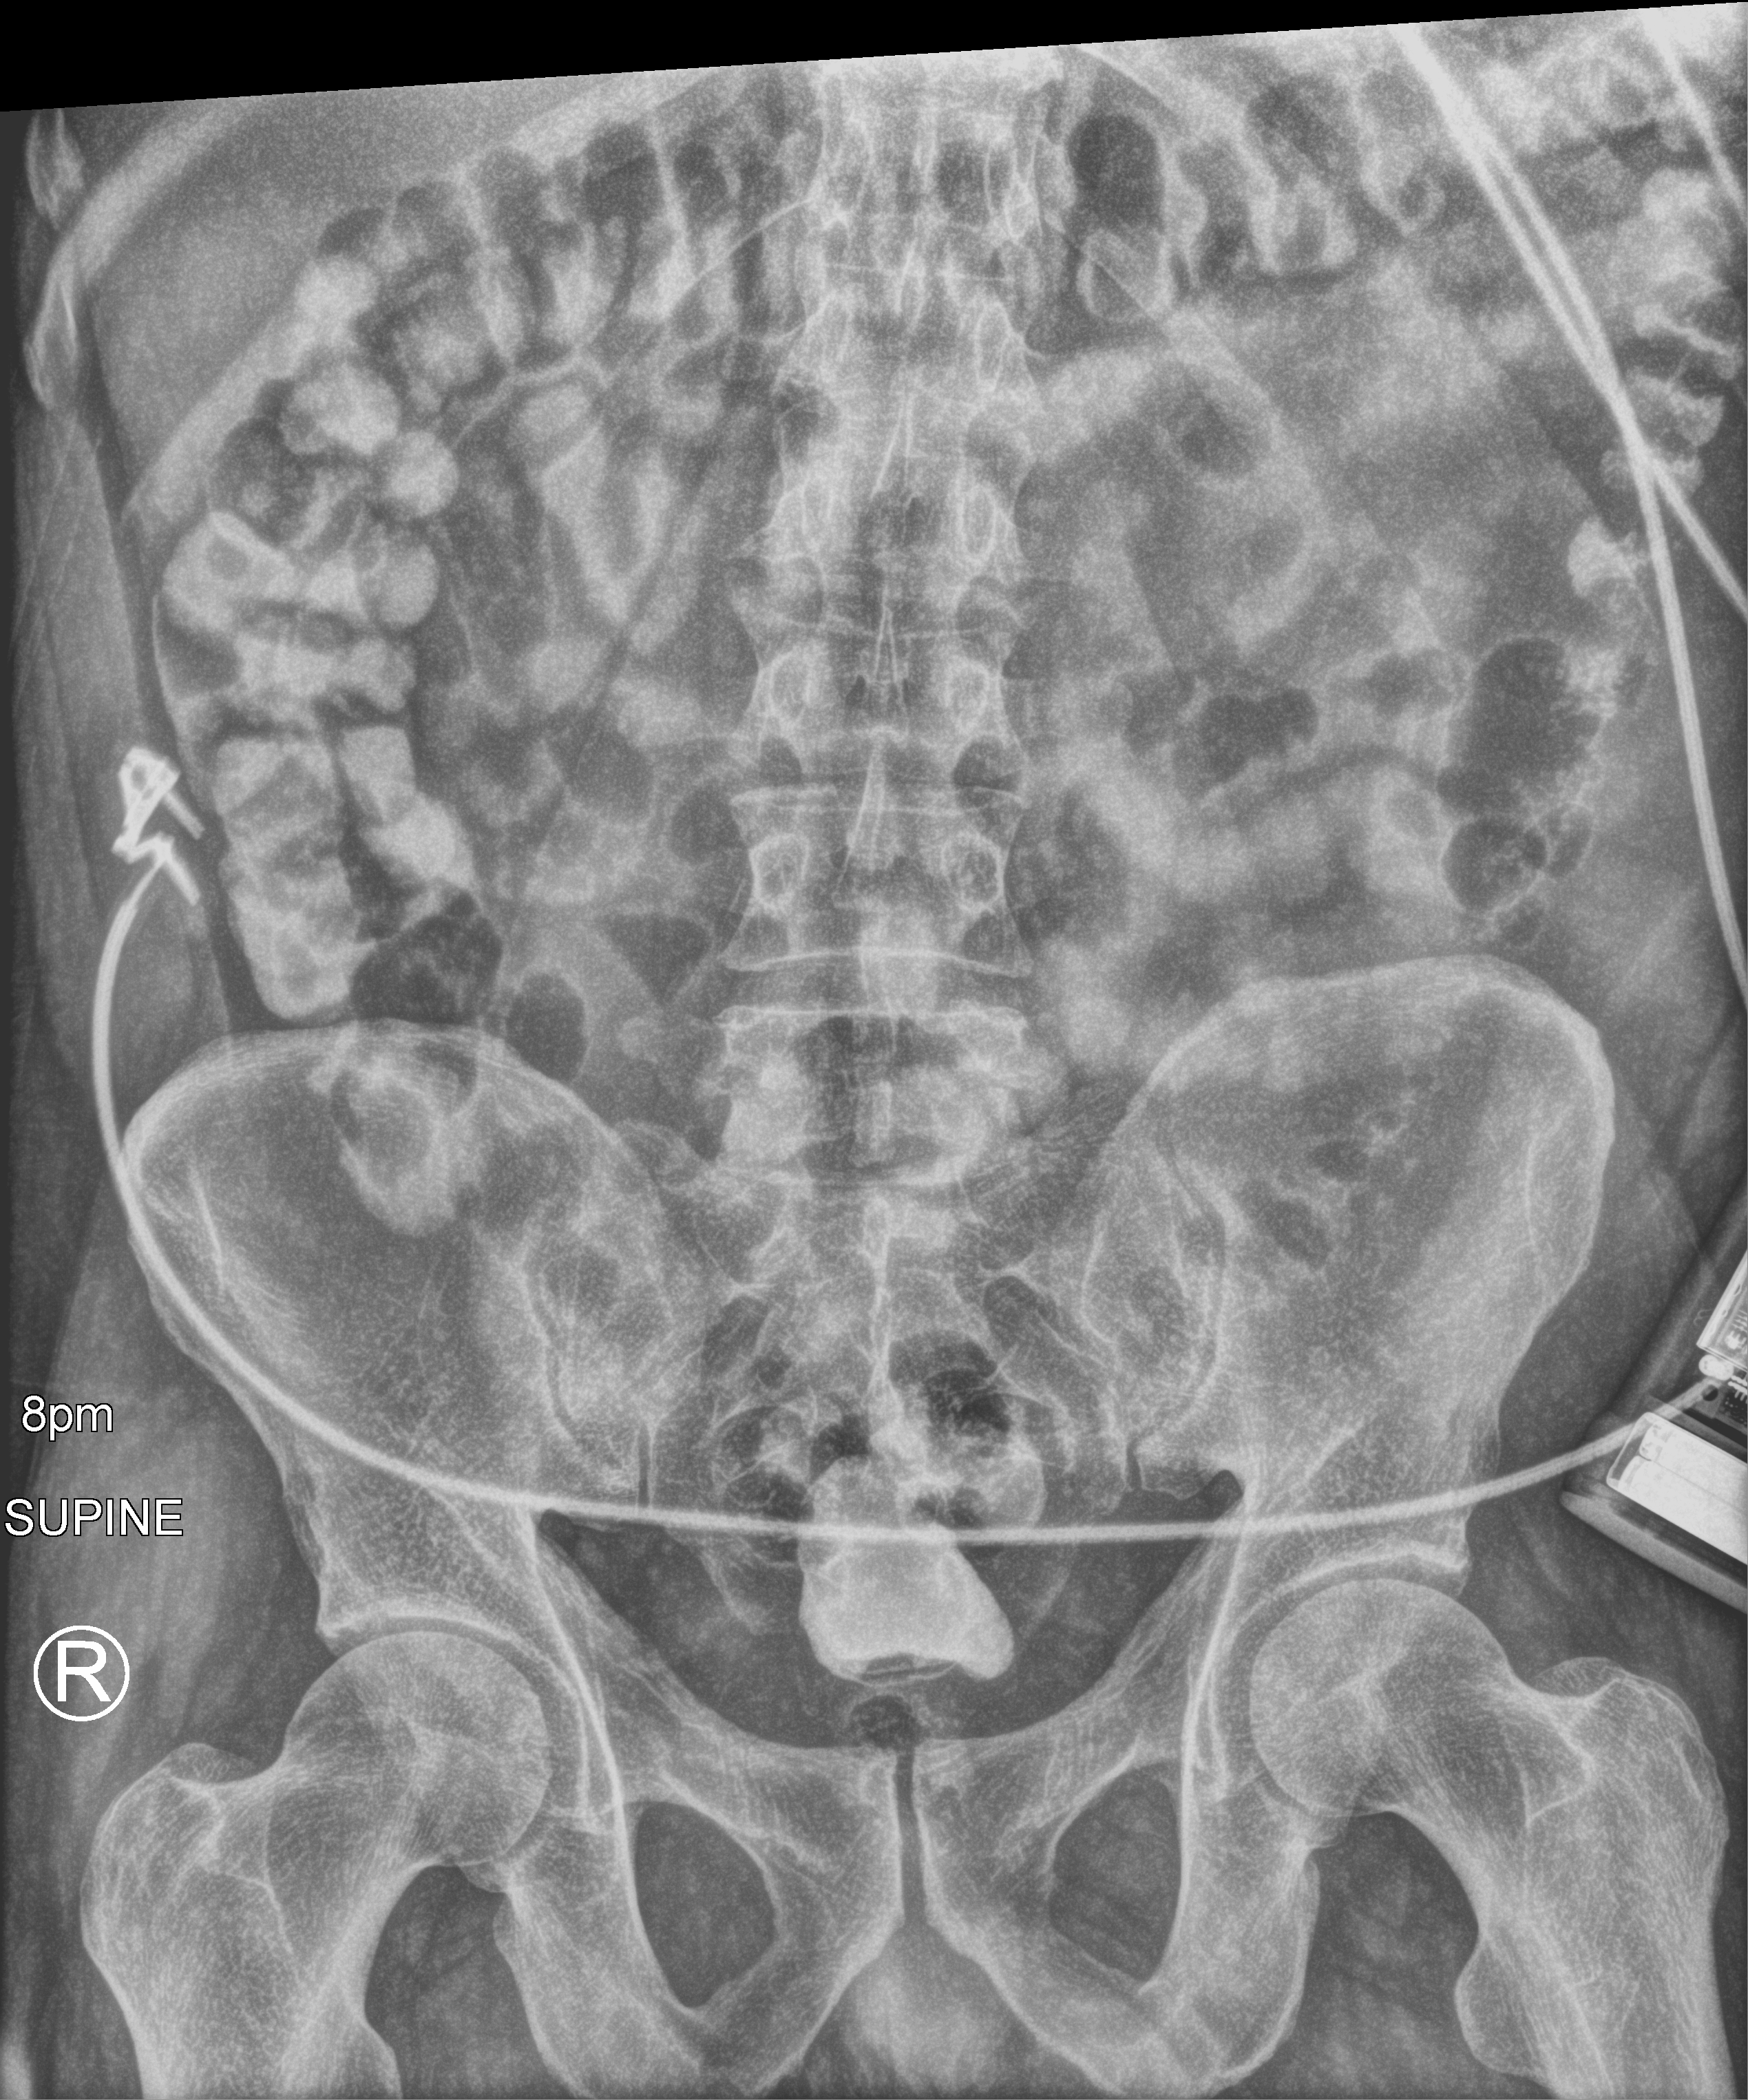
Abdomen X-ray (portable), anteroposterior (AP) projection. Male patient hospitalised with COVID-19, age 18–59 years.
Hospital-stay facts (about this admission, not read from this image; timing relative to this image not recorded): admitted to intensive care during this hospital stay: no; length of hospital stay: 4 days.